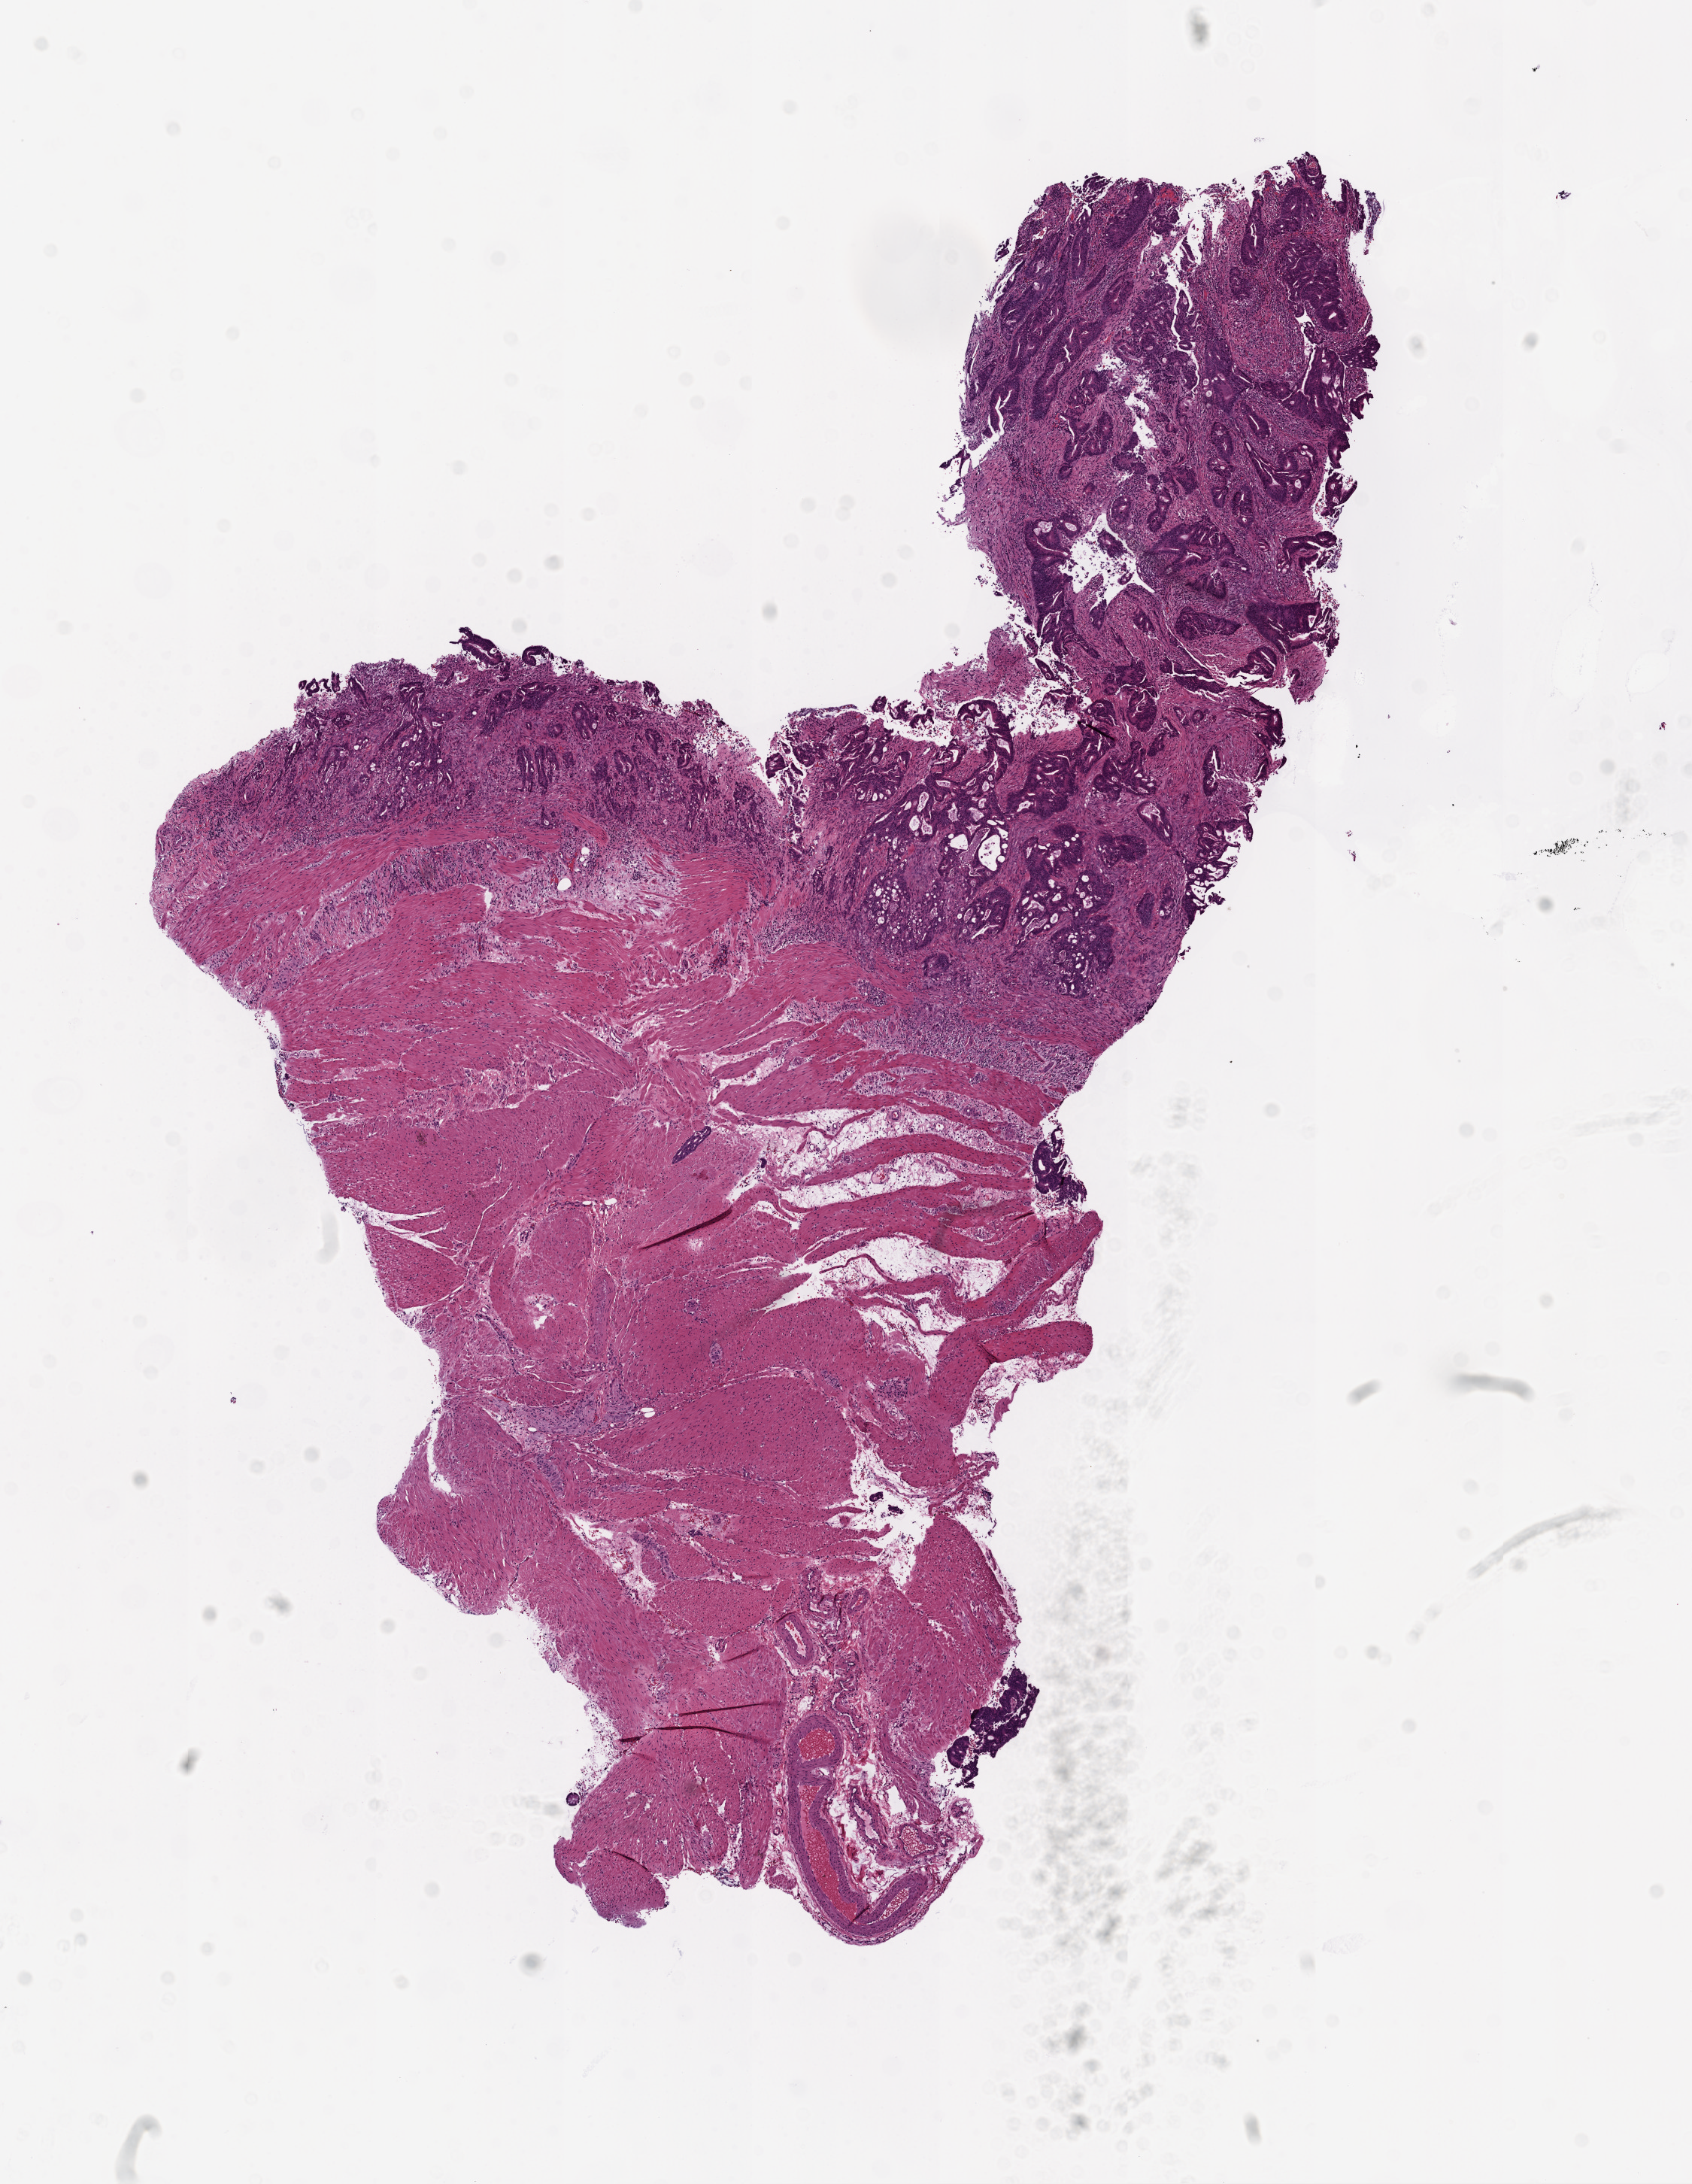
Digitized Hematoxylin and eosin (H&E) stained tissue section (whole slide), low-resolution overview of the scanned area, about 9.0 x 11.7 mm (acquisition: 20x scan). Frozen section. Primary tumour sample from the colon. Female patient; age at initial diagnosis 75 years. Composition of this section per pathologist review: tumour cells 59%, tumour nuclei 70%, normal cells 50%, stromal cells 10%, necrosis 1%.
TNM: T2 N0 M0. AJCC pathologic stage: I. Histologic diagnosis: Adenocarcinoma, NOS. Lymph nodes positive (case pathology): 0 of 33 examined.